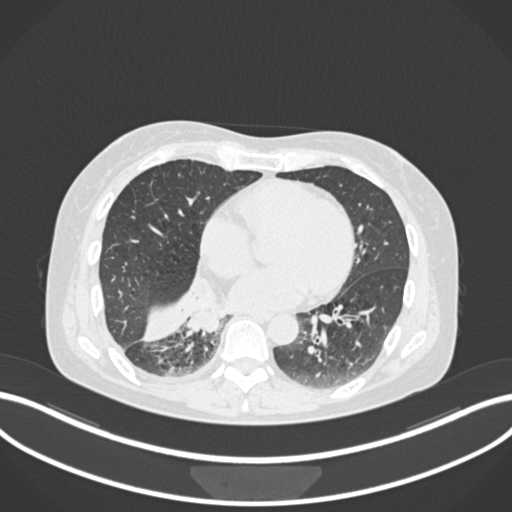
Chest CT, one axial slice; slice 61 of 168 in the series (ordered by position); reconstruction kernel B30f; 120 kVp; lung window (W 1500 / L -600 HU); 1 mm slice thickness; 512 × 512 image matrix, field of view 400 × 400 mm. Female patient, age 63 years. Case-level facts recorded for this patient, not image findings: clinical TNM (as recorded): T1c N0 M0.
Outlined on this slice (rectangle marked by the reading radiologist):
- lung tumour (recorded histology: adenocarcinoma): bounding box [x1, y1, x2, y2] px = [182, 296, 230, 336]